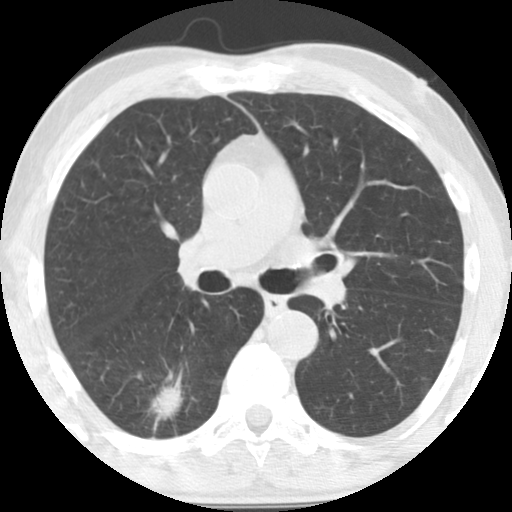
Low-dose screening chest CT, axial slice; baseline screening round; lung window (W 1500 / L -600 HU); 2.5 mm slice thickness; 512 × 512 image matrix. Male participant, aged 64 years at enrolment.
• Expert-annotated lung lesion, bounding box (x1, y1, x2, y2) in pixels: (116, 366, 189, 432).
• Reader record for this screening exam (exam-level; its link to the box is not recorded): non-calcified nodule or mass ≥4 mm, right lower lobe, 36 × 26 mm, spiculated (stellate) margins, soft tissue attenuation.
• Official screen result: positive, change unspecified: nodule(s) >= 4 mm or enlarging nodule(s), mass(es), or other non-specific abnormalities suspicious for lung cancer.